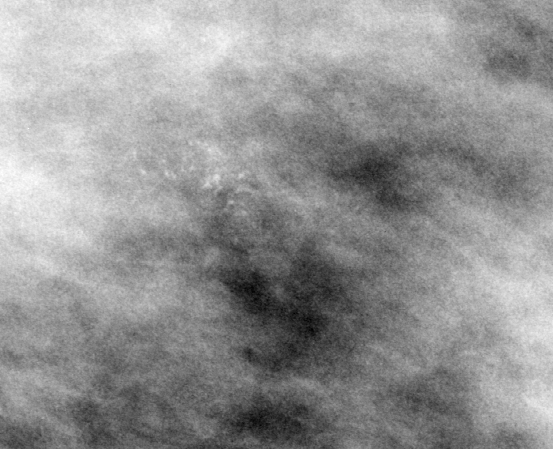
Cropped region of a digitized screen-film mammogram centred on a radiologist-marked abnormality; left breast; CC view; BI-RADS breast density category 2 (scale 1–4).
Calcifications, morphology pleomorphic, distribution clustered; BI-RADS assessment category 5; pathology result (as recorded, not read from the image): malignant.